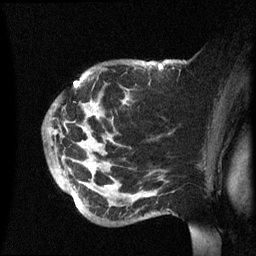
Breast MRI (dynamic contrast-enhanced), one sagittal slice; slice 43 of 60 in the series (ordered by position); dynamic contrast-enhanced series, image 2 of 3 at this slice position (ordered by acquisition); 1.5 T; TE 4.2 ms, TR 8.4 ms; 2.4 mm slice thickness; 256 × 256 image matrix, field of view 230 × 230 mm. Patient: female, 49 years.
Structures marked on this image (semi-automatically segmented with operator editing):
- analysis volume of interest (the breast-tissue region the enhancement analysis was run in; not a lesion): bounding box (x1, y1, x2, y2) in pixels: (43, 60, 174, 225)
- tumour enhancement mask (voxels above the 70 % enhancement threshold inside the analysis volume of interest): (96, 64, 163, 118)